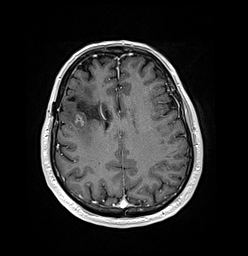
Brain MRI from a brain-tumour surgery series, one axial slice; slice 59 of 176 in the series (ordered by position); T1-weighted post-contrast; 1 mm slice thickness; 248 × 256 image matrix, field of view 242 × 250 mm. Case-level facts recorded for this patient, not image findings: histopathology: Oligodendroglioma; WHO grade: 3; IDH mutation: yes; tumour location: Right Frontal.
Outlined on this slice (manually delineated by an expert):
- previous resection cavity: bounding box (x1, y1, x2, y2) in pixels: (70, 98, 75, 101)
- tumour: (73, 112, 85, 127)